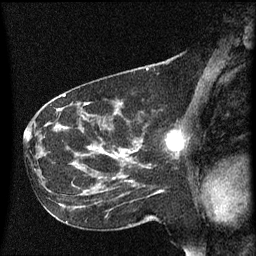
Breast MRI (dynamic contrast-enhanced), one sagittal slice; position 31 of 60 along the scan axis; dynamic contrast-enhanced series, image 2 of 3 at this slice position (ordered by acquisition); 1.5 T; TE 4.2 ms, TR 8.4 ms; 2 mm slice thickness; 256 × 256 image matrix, field of view 200 × 200 mm. Female patient, age 41 years. From the clinical record (not read from this slice): setting: breast cancer imaged before/during neoadjuvant chemotherapy; receptor status: triple-negative.
Structures marked on this image (semi-automatically segmented with operator editing):
- analysis volume of interest (the breast-tissue region the enhancement analysis was run in; not a lesion): bounding box [x1, y1, x2, y2] px = [138, 132, 182, 159]
- tumour enhancement mask (voxels above the 70 % enhancement threshold inside the analysis volume of interest): [168, 134, 182, 151]